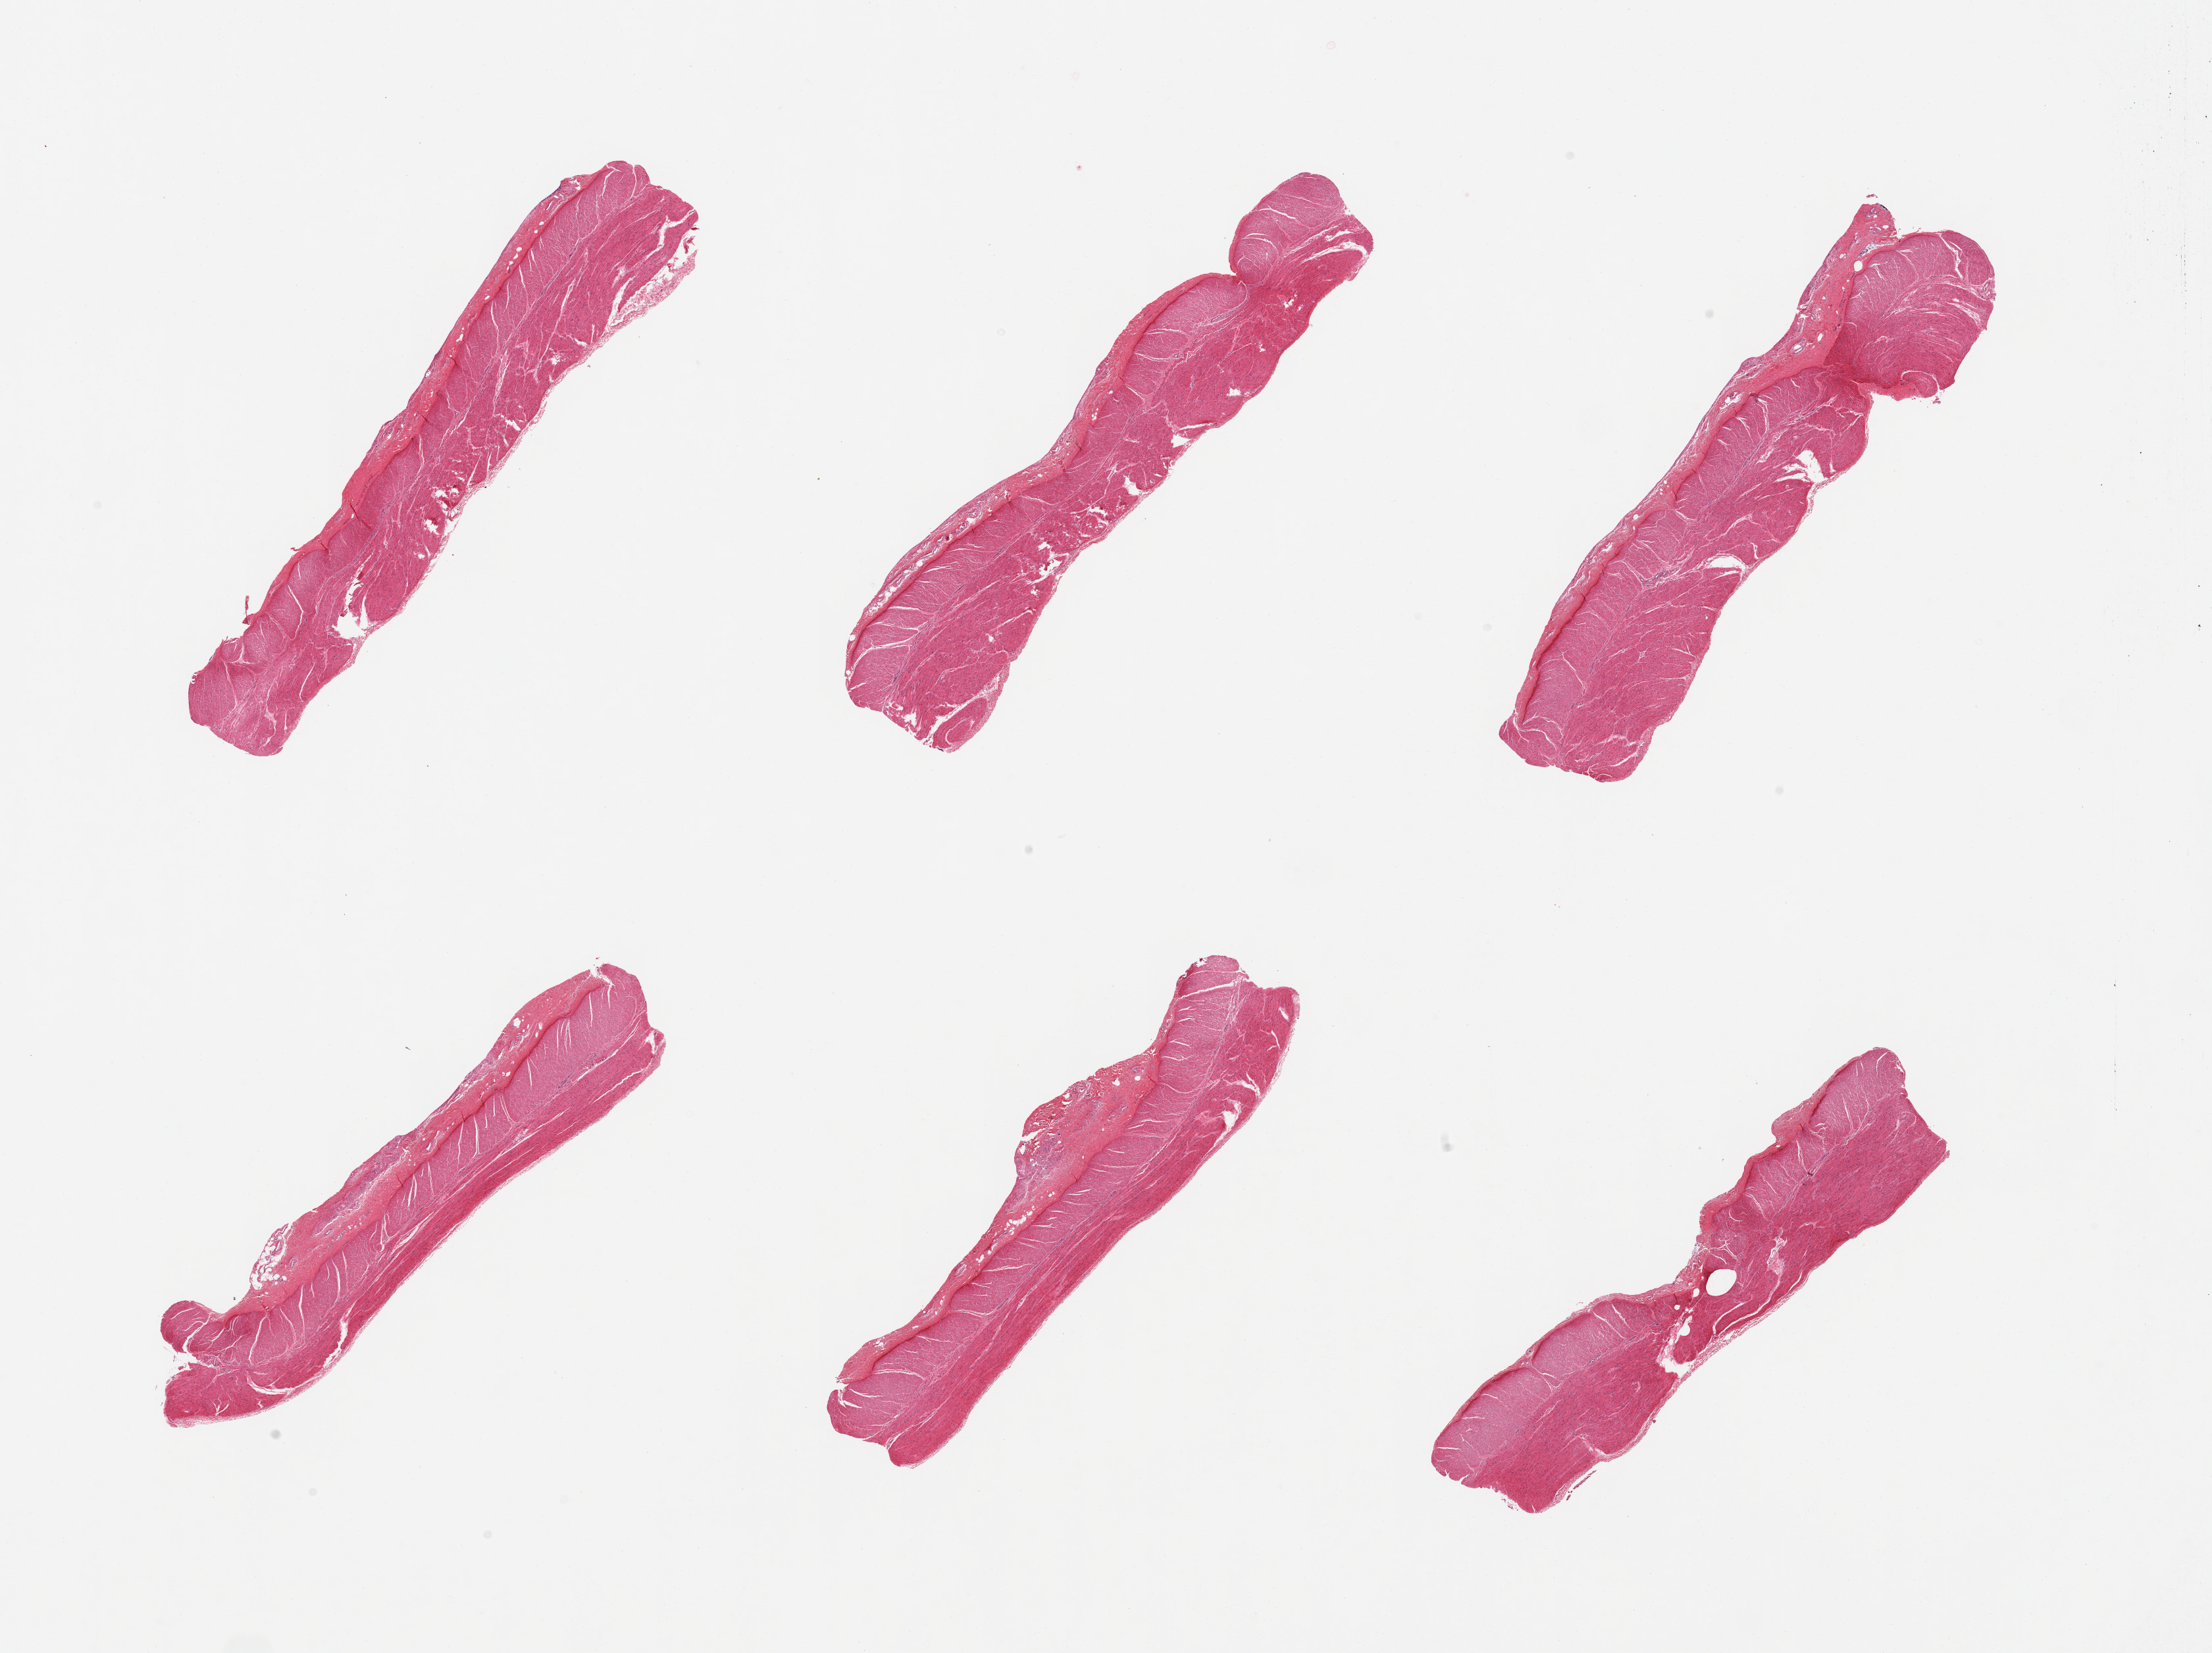
H&E whole-slide image, brightfield, a low-resolution overview of the entire scanned area, about 26.6 x 19.9 mm, PAXgene-fixed paraffin-embedded (PFPE) section, sampled site (target tissue): sigmoid colon, donor tissue sample. Male donor.
Review note (as recorded): 6 pieces; attached serosa measures up to 1mm.